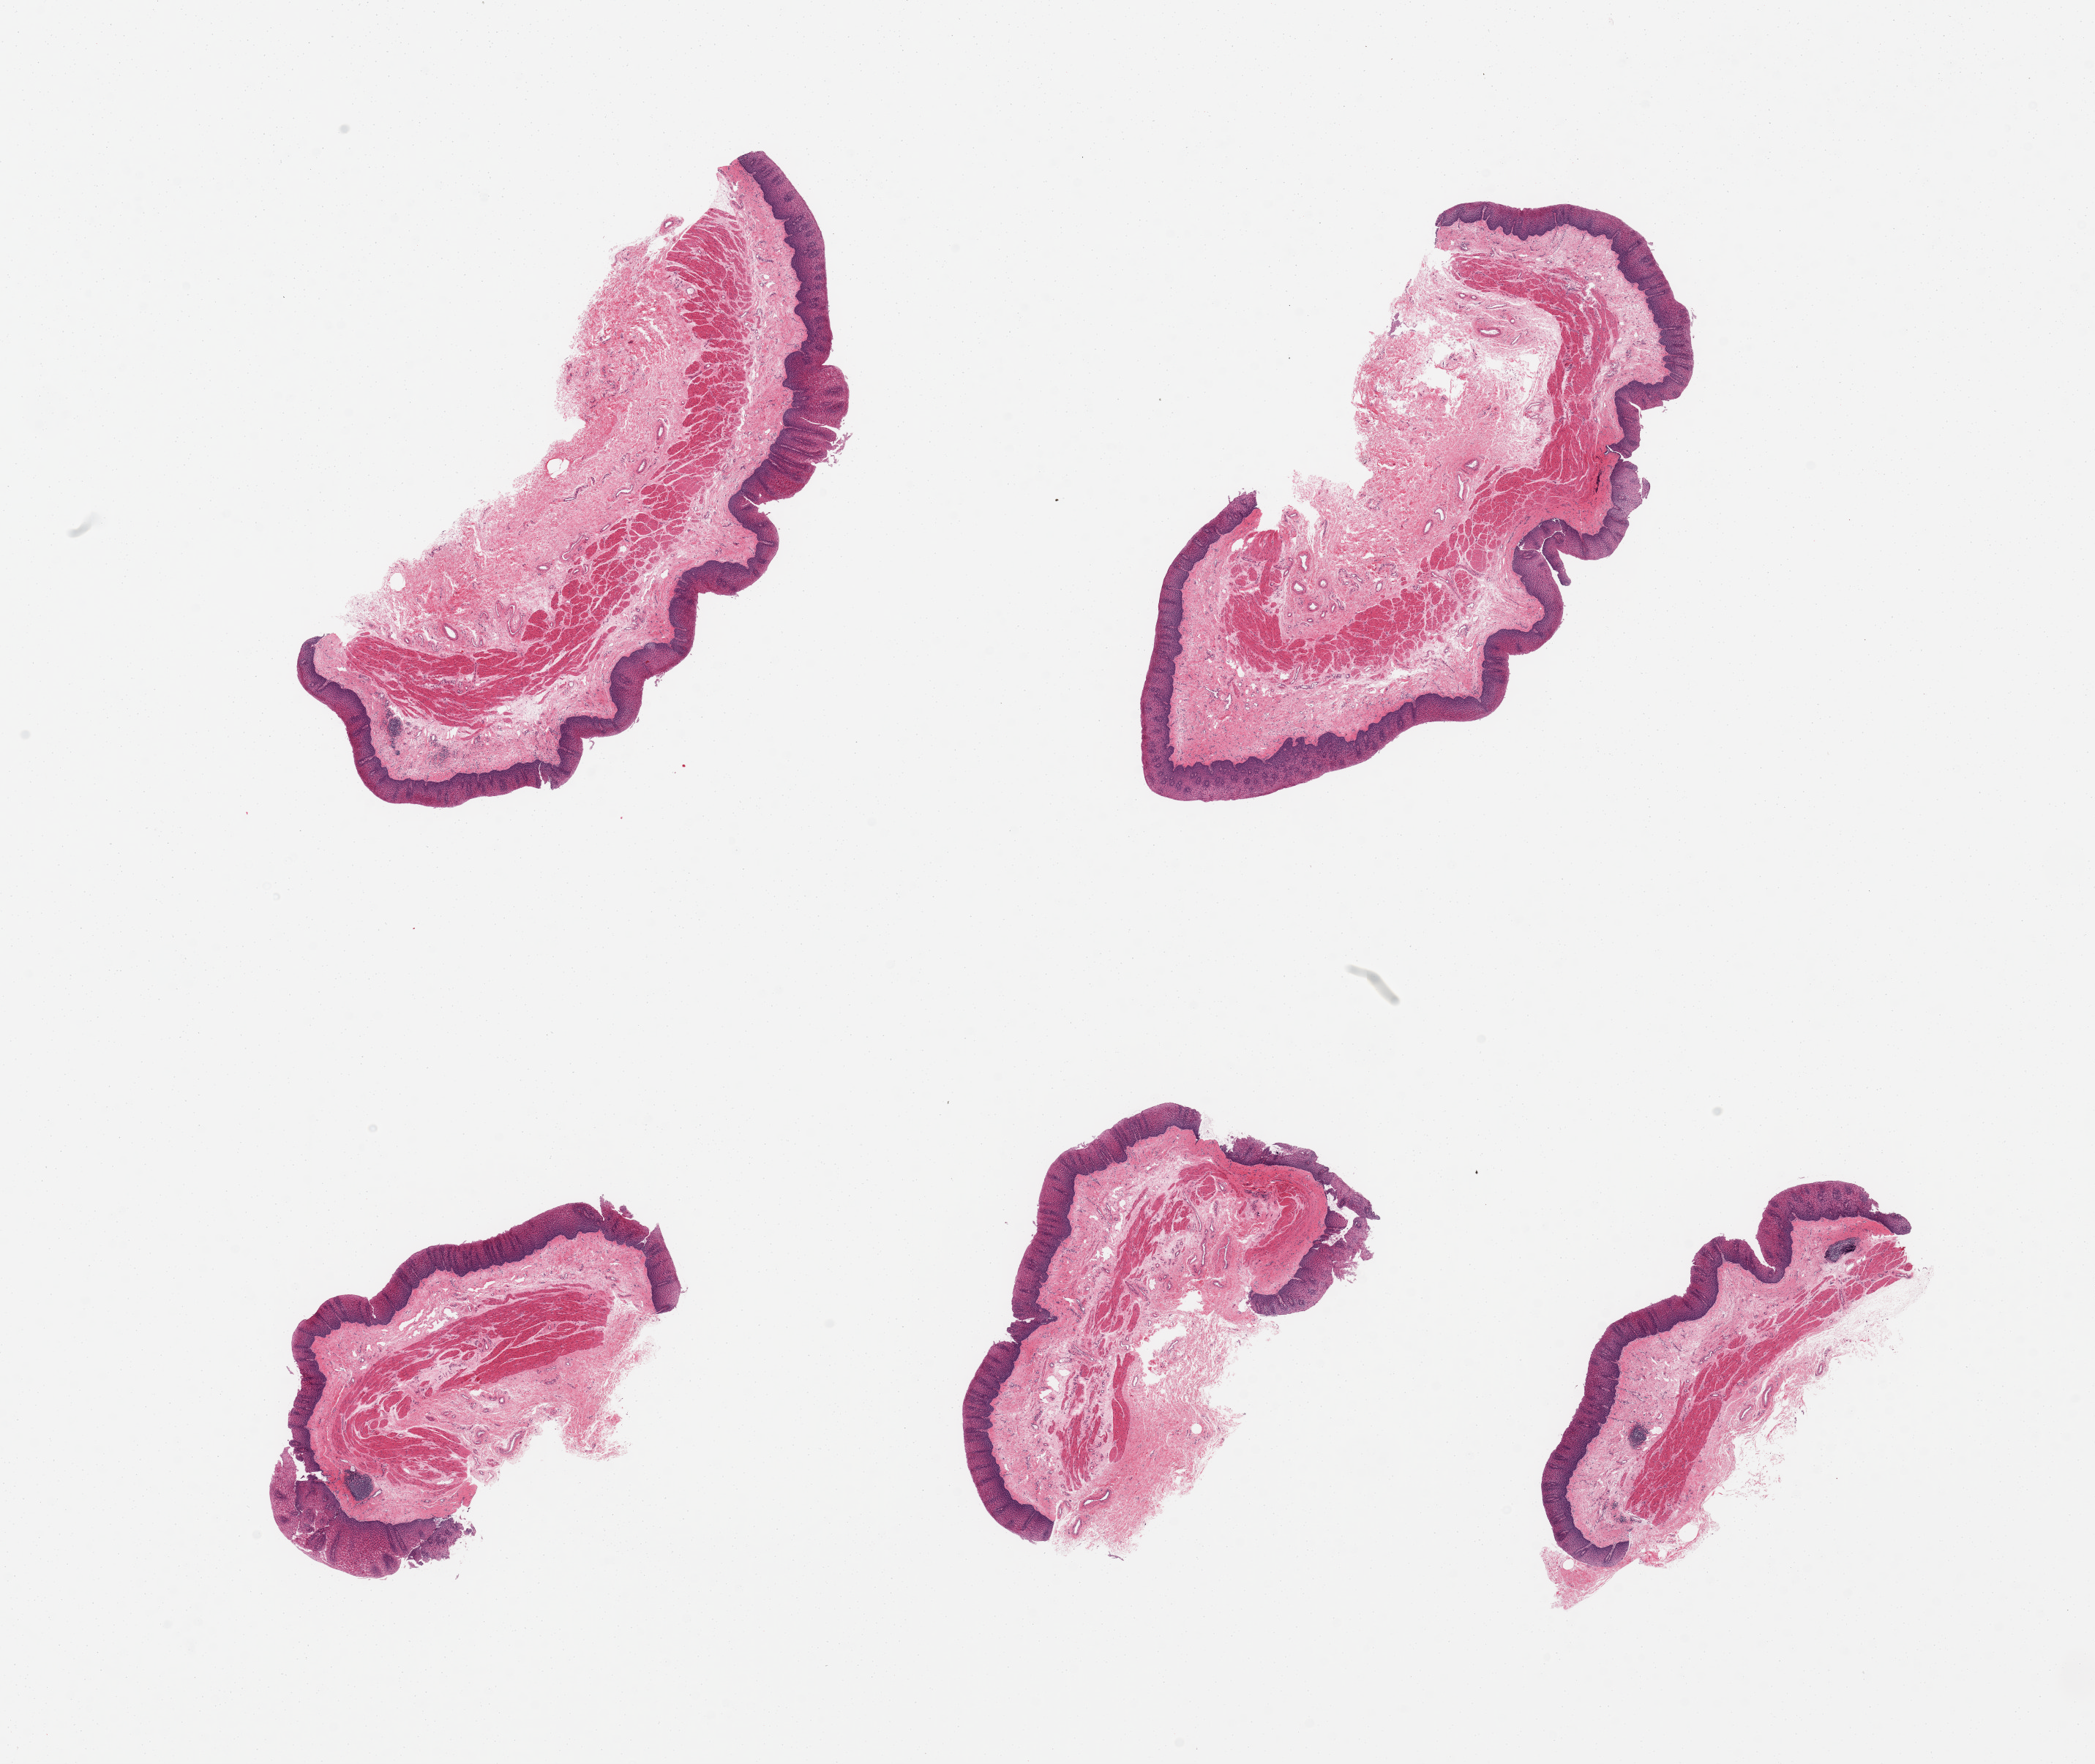
H&E whole-slide image, low-resolution overview of the scanned area, about 22.6 x 19.1 mm, PAXgene-fixed paraffin-embedded (PFPE) section, target tissue: esophageal mucous membrane, tissue donor sample.
Review note (as recorded): 5 pieces.